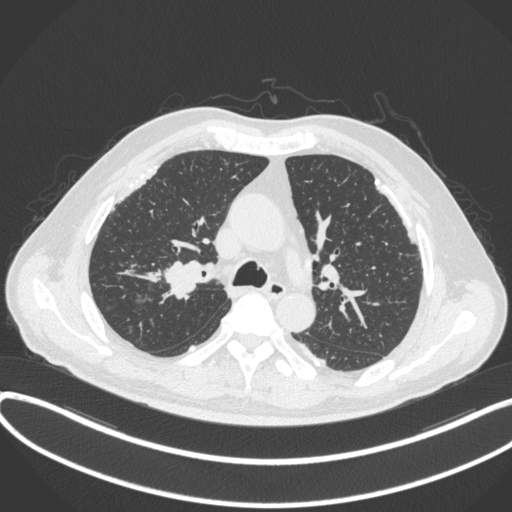
Chest CT, one axial slice; position 285 of 455 along the scan axis; lung window (W 1500 / L -600 HU); 1 mm slice thickness; 512 × 512 image matrix, field of view 400 × 400 mm. Male patient, age 58 years. From the clinical record (not read from this slice): clinical TNM (as recorded): T1c N0 M0.
Structures marked on this image (rectangle marked by the reading radiologist):
- lung tumour (recorded histology: squamous cell carcinoma): bounding box (x1, y1, x2, y2) in pixels: (160, 254, 207, 303)